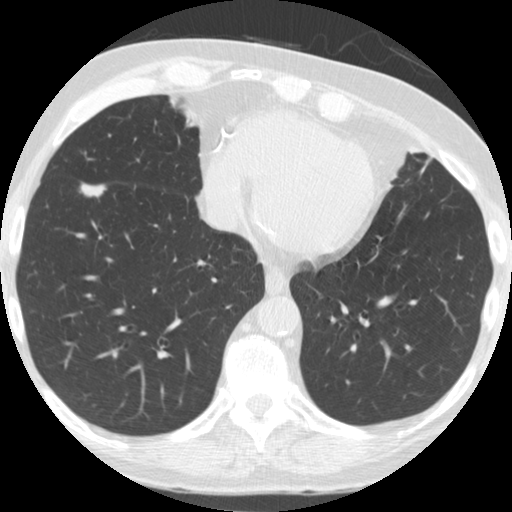
Low-dose screening chest CT, one axial slice. Position 70 of 182 along the scan axis. Reconstruction kernel STANDARD. 120 kVp. Lung window (W 1500 / L -600 HU). 2.5 mm slice thickness. 512 × 512 image matrix, field of view 320 × 320 mm.
Outlined on this slice (outlined manually by an expert reader):
- lesion 1 (tumor, lower lobe of right lung): bounding box (x1, y1, x2, y2) in pixels: (80, 183, 106, 198)